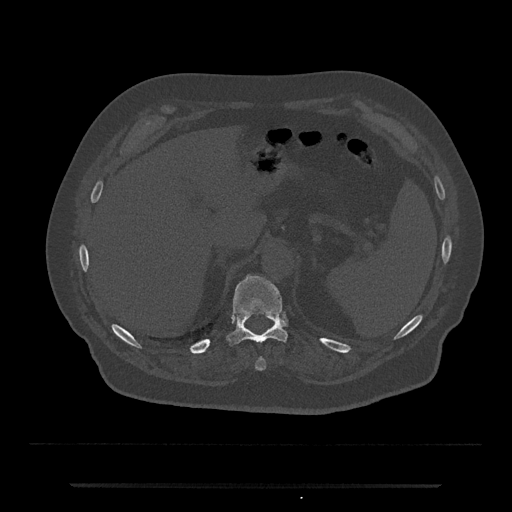
CT including the spine, one axial slice; position 654 of 797 along the scan axis; reconstruction kernel Br40s/3; 120 kVp; bone window (W 1800 / L 400 HU); 512 × 512 image matrix, field of view 434 × 434 mm. Patient: male, 80 years. Case-level facts recorded for this patient, not image findings: primary cancer: prostate.
Outlined on this slice (semi-automatically segmented with operator editing):
- T10 vertebra: bounding box <255,357,266,370> (left, top, right, bottom; pixels)
- T11 vertebra: <227,274,287,345>